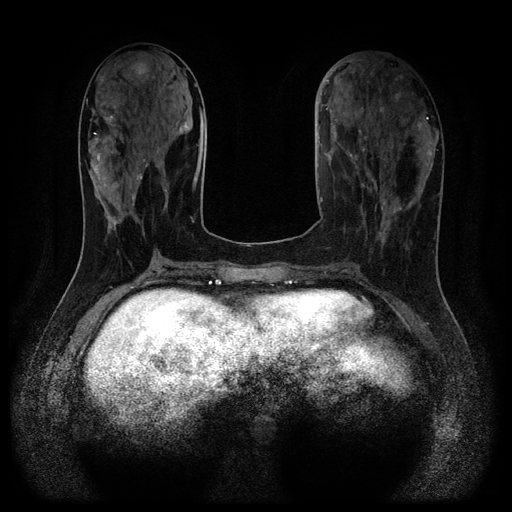
Breast MRI (dynamic contrast-enhanced, multi-phase), one axial slice; slice 43 of 116 in the series (ordered by position); dynamic contrast-enhanced series, time point 2 of 5 at this slice position (early post-contrast); 1.5 T; TE 2.7 ms, TR 5.4 ms; 2.2 mm slice thickness; 512 × 512 image matrix. Patient: female, 43 years.
Annotated regions visible in this slice (semi-automatically segmented with operator editing):
- breast lesion (labelled benign in the annotation): bounding box (x1, y1, x2, y2) in pixels: (128, 62, 149, 76)